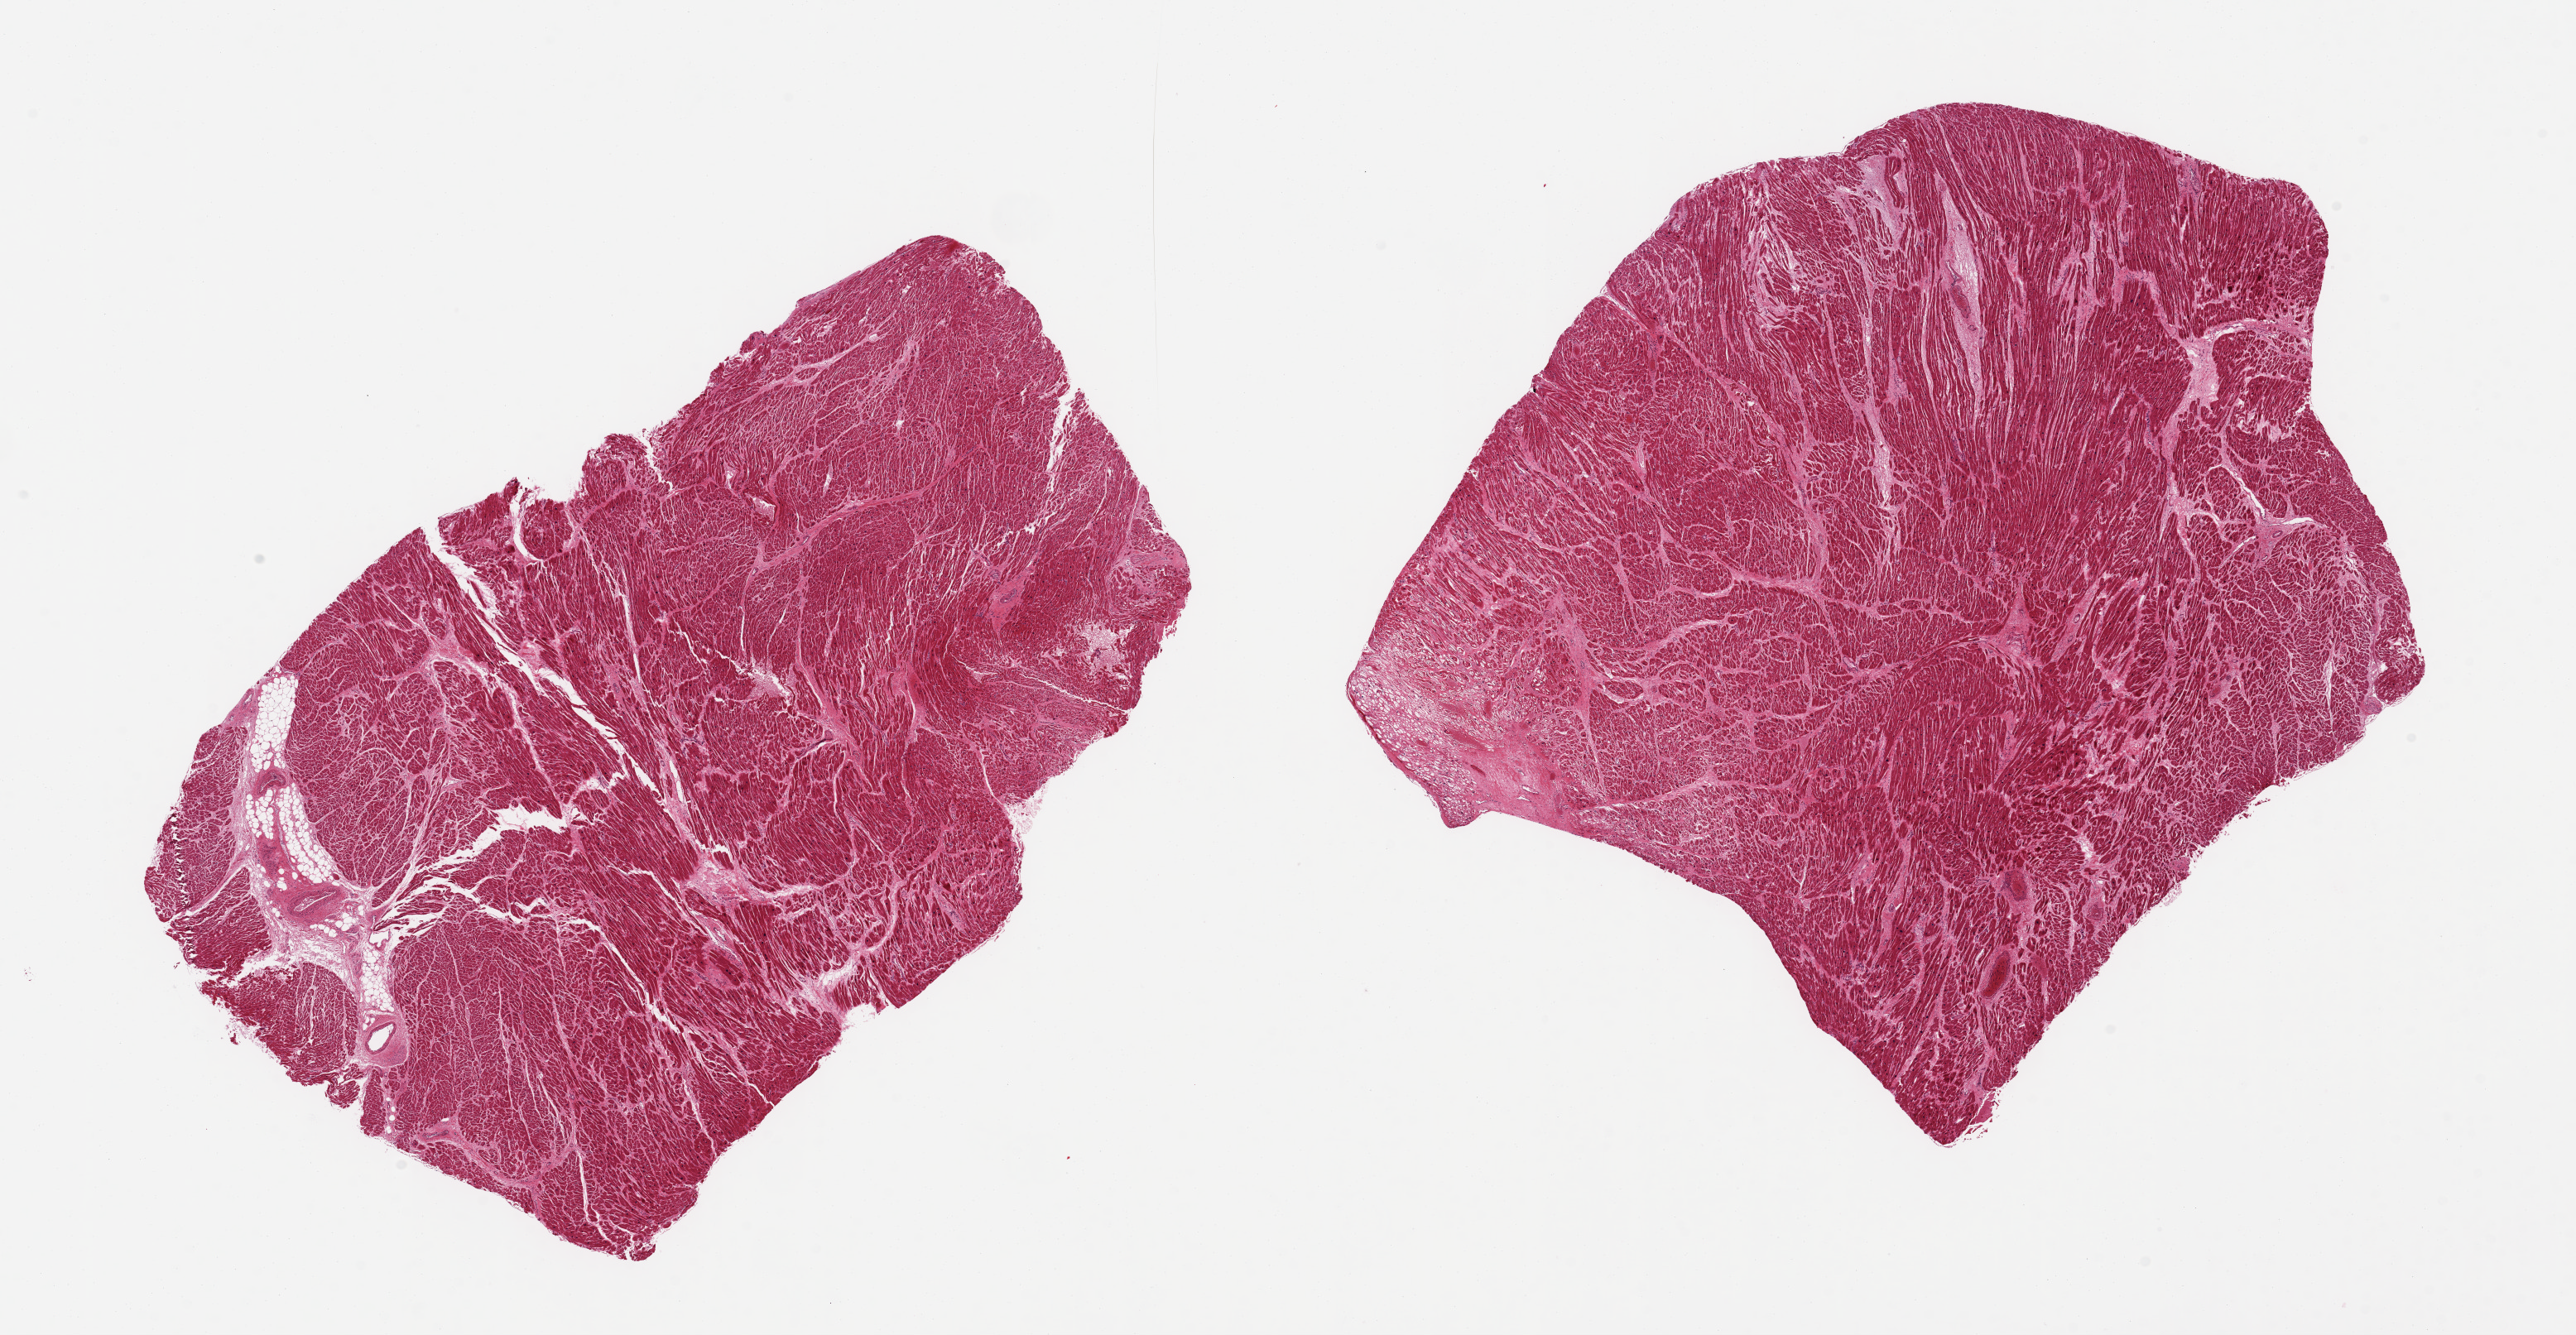
Whole-slide image, H&E stain, brightfield — whole scanned area (about 24.6 x 12.8 mm) shown as a low-resolution overview. PAXgene-fixed paraffin-embedded (PFPE) section. Sampled site (target tissue): heart. Donor tissue sample.
Pathologist's review note for this sample: 2 pieces; 1 with a 0.6 sq mm scar adjacent to a 4 sq mm zone of vacuolated myofibers all consistent with previous ischemic damage.